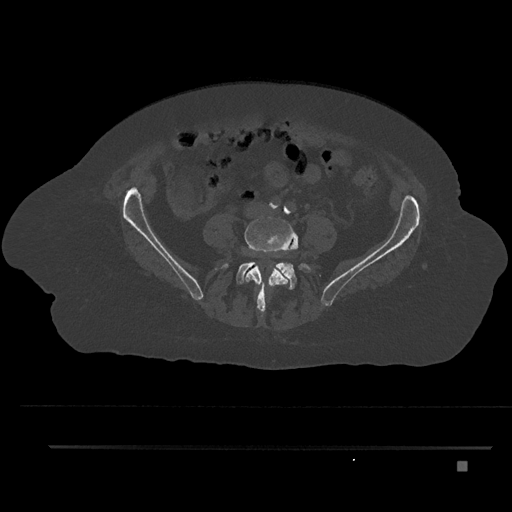
CT including the spine, one axial slice. Slice 61 of 797 in the series (ordered by position). Bone window (W 1800 / L 400 HU). 0.5 mm slice thickness. 512 × 512 image matrix, field of view 437 × 437 mm. Female patient, age 76 years. From the clinical record (not read from this slice): primary cancer: lung; vertebrae with lytic lesions (as recorded): T11, L3.
Outlined on this slice (semi-automatically segmented with operator editing):
- L4 vertebra: bounding box (x1, y1, x2, y2) in pixels: (245, 217, 298, 313)
- L5 vertebra: (222, 246, 311, 290)